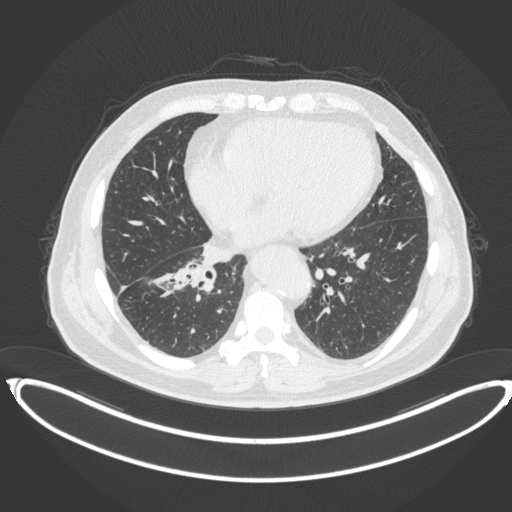
Chest CT, one axial slice. Slice 159 of 383 in the series (ordered by position). Reconstruction kernel B31f. Lung window (W 1500 / L -600 HU). 1 mm slice thickness. 512 × 512 image matrix, field of view 448 × 448 mm. Patient: male, 61 years. Case-level facts recorded for this patient, not image findings: clinical TNM (as recorded): T1b N1 M0.
Structures marked on this image (bounding box drawn by a radiologist):
- lung tumour (recorded histology: squamous cell carcinoma): bounding box (x1, y1, x2, y2) in pixels: (170, 255, 222, 296)